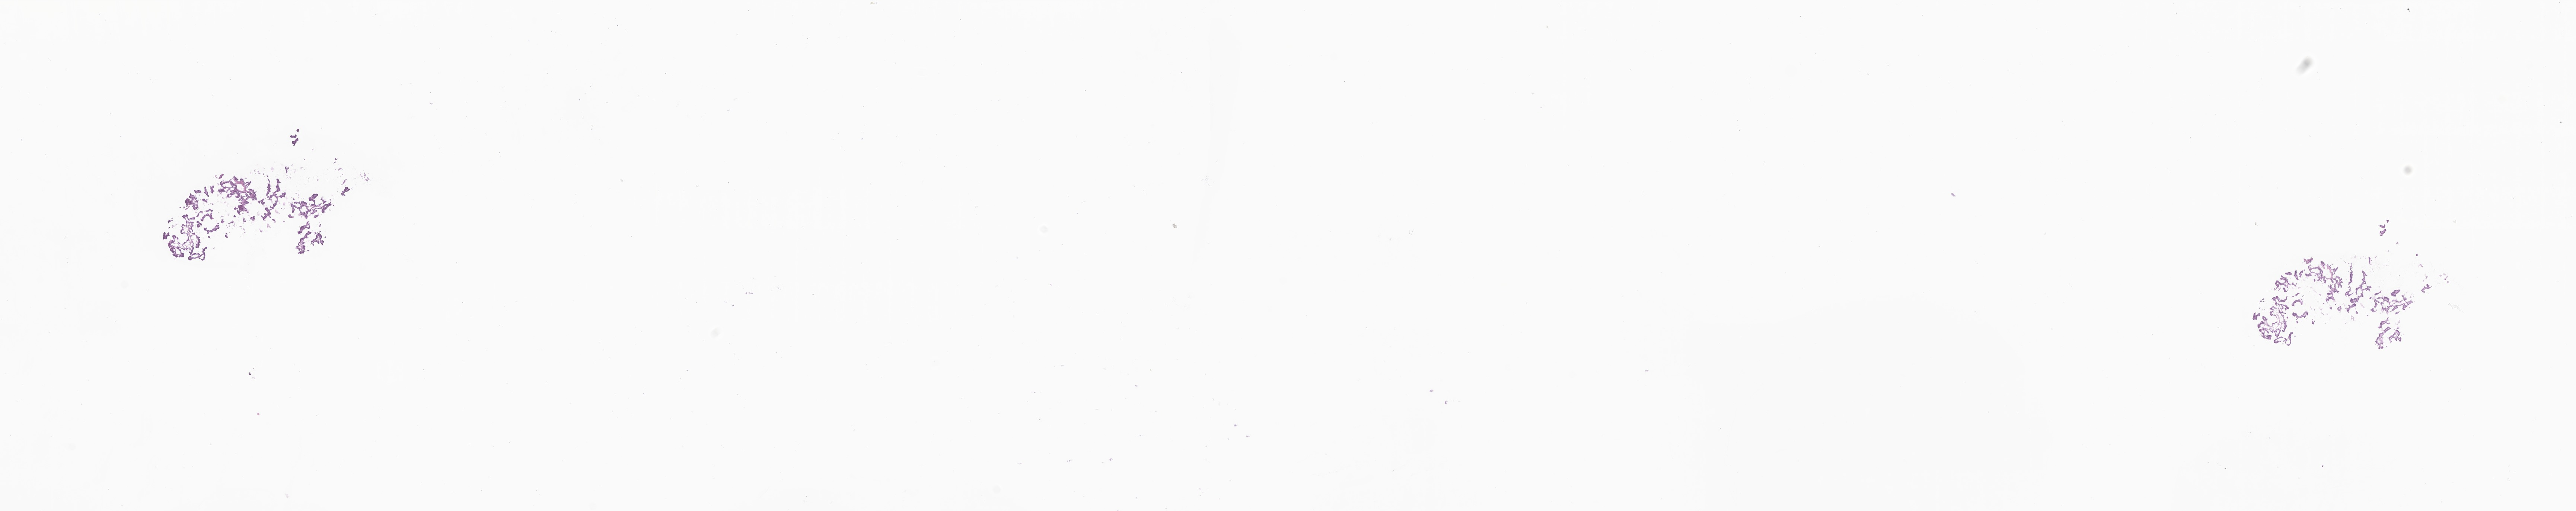
Digitized H&E-stained section of tumor tissue from the brain — a low-resolution overview of the entire scanned area, about 29.2 x 5.8 mm, frozen section. Patient male; age 157 days.
Diagnosis: Choroid plexus papilloma, NOS.